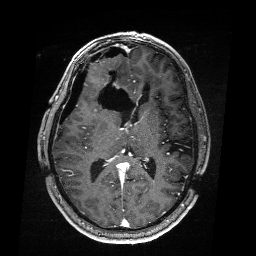
Brain MRI from a brain-tumour surgery series, one axial slice; slice 99 of 176 in the series (ordered by position); T1-weighted post-contrast; 256 × 256 image matrix. From the clinical record (not read from this slice): histopathology: Astrocytoma; WHO grade: 4; IDH mutation: yes.
Outlined on this slice (outlined manually by an expert reader):
- residual tumour: bounding box [x1, y1, x2, y2] px = [107, 82, 118, 136]